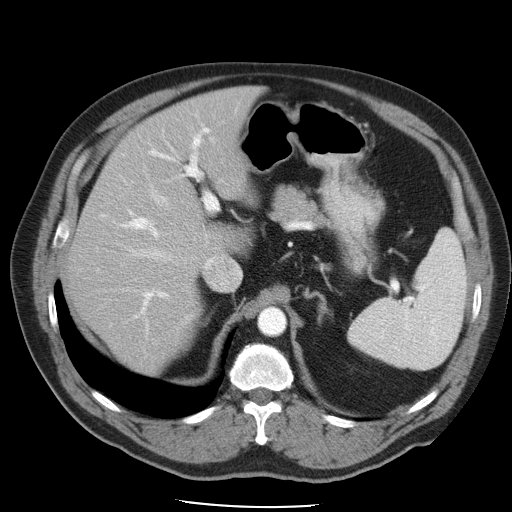
Contrast-enhanced abdominal CT, one axial slice; 120 kVp; intravenous contrast given; soft-tissue window (W 400 / L 40 HU); 5 mm slice thickness; 512 × 512 image matrix. Male patient, age 68 years. From the clinical record (not read from this slice): diagnosis: colorectal cancer liver metastases, imaged before liver resection; multiple liver metastases: yes; largest metastasis: 1.7 cm; disease in both lobes: no.
Outlined on this slice (outlined manually by an expert reader):
- hepatic veins: bounding box <117,165,241,292> (left, top, right, bottom; pixels)
- liver: <68,88,257,372>
- planned liver remnant (the part of the liver to remain after resection): <68,88,256,372>
- portal vein (with intrahepatic branches): <121,111,237,319>